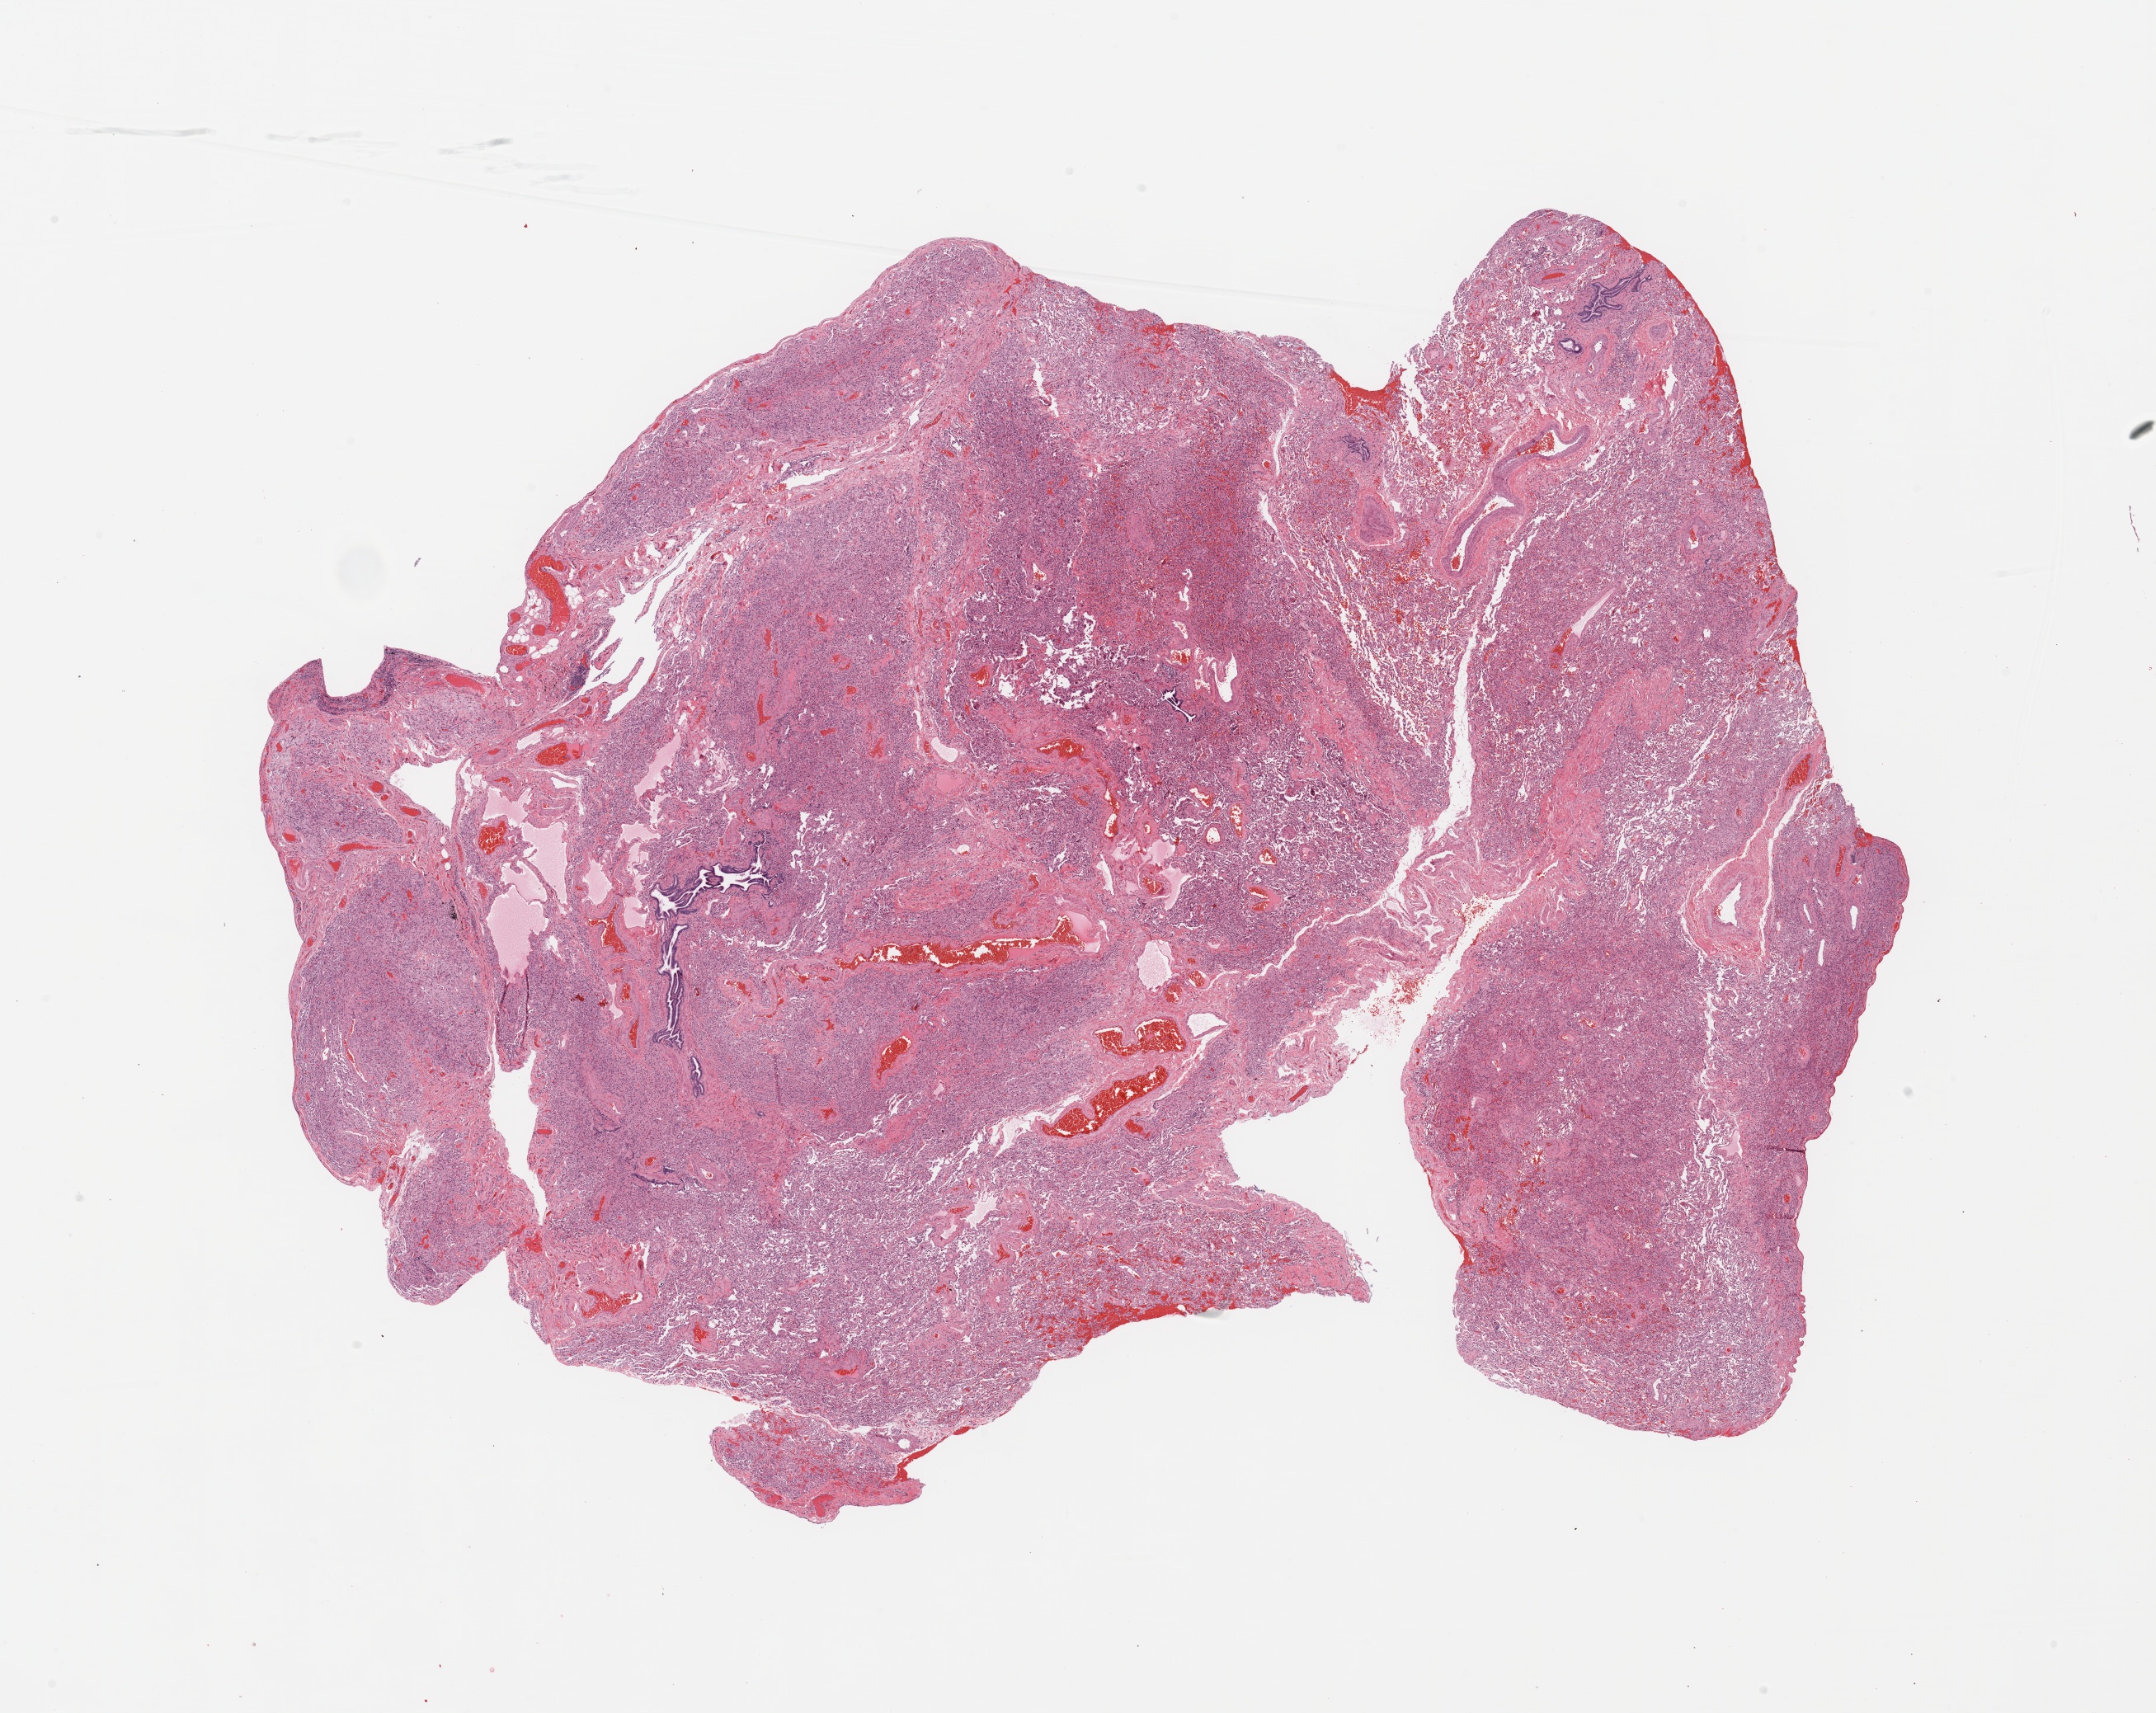
Digitized H&E-stained tissue section (whole slide) — low-resolution overview of the scanned area, about 20.7 x 16.4 mm (slide scanned at 20x), normal (non-tumour) tissue sample, lung. Male, 77 y/o.
This section: normal (non-tumour) tissue from the same patient. Patient diagnosis: Adenocarcinoma, NOS.